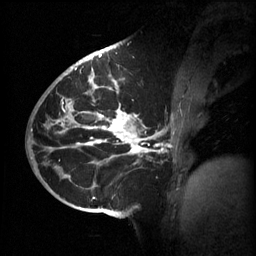
Breast MRI (dynamic contrast-enhanced), one sagittal slice; position 31 of 60 along the scan axis; 3 images stored at this slice position (order not interpretable as contrast timing); 1.5 T; TE 4.2 ms, TR 11 ms; 2 mm slice thickness; 256 × 256 image matrix, field of view 220 × 220 mm. Patient: female, 51 years.
Annotated regions visible in this slice (semi-automatically segmented with operator editing):
- analysis volume of interest (the breast-tissue region the enhancement analysis was run in; not a lesion): bounding box (x1, y1, x2, y2) in pixels: (63, 80, 176, 201)
- tumour enhancement mask (voxels above the 70 % enhancement threshold inside the analysis volume of interest): (63, 80, 164, 199)